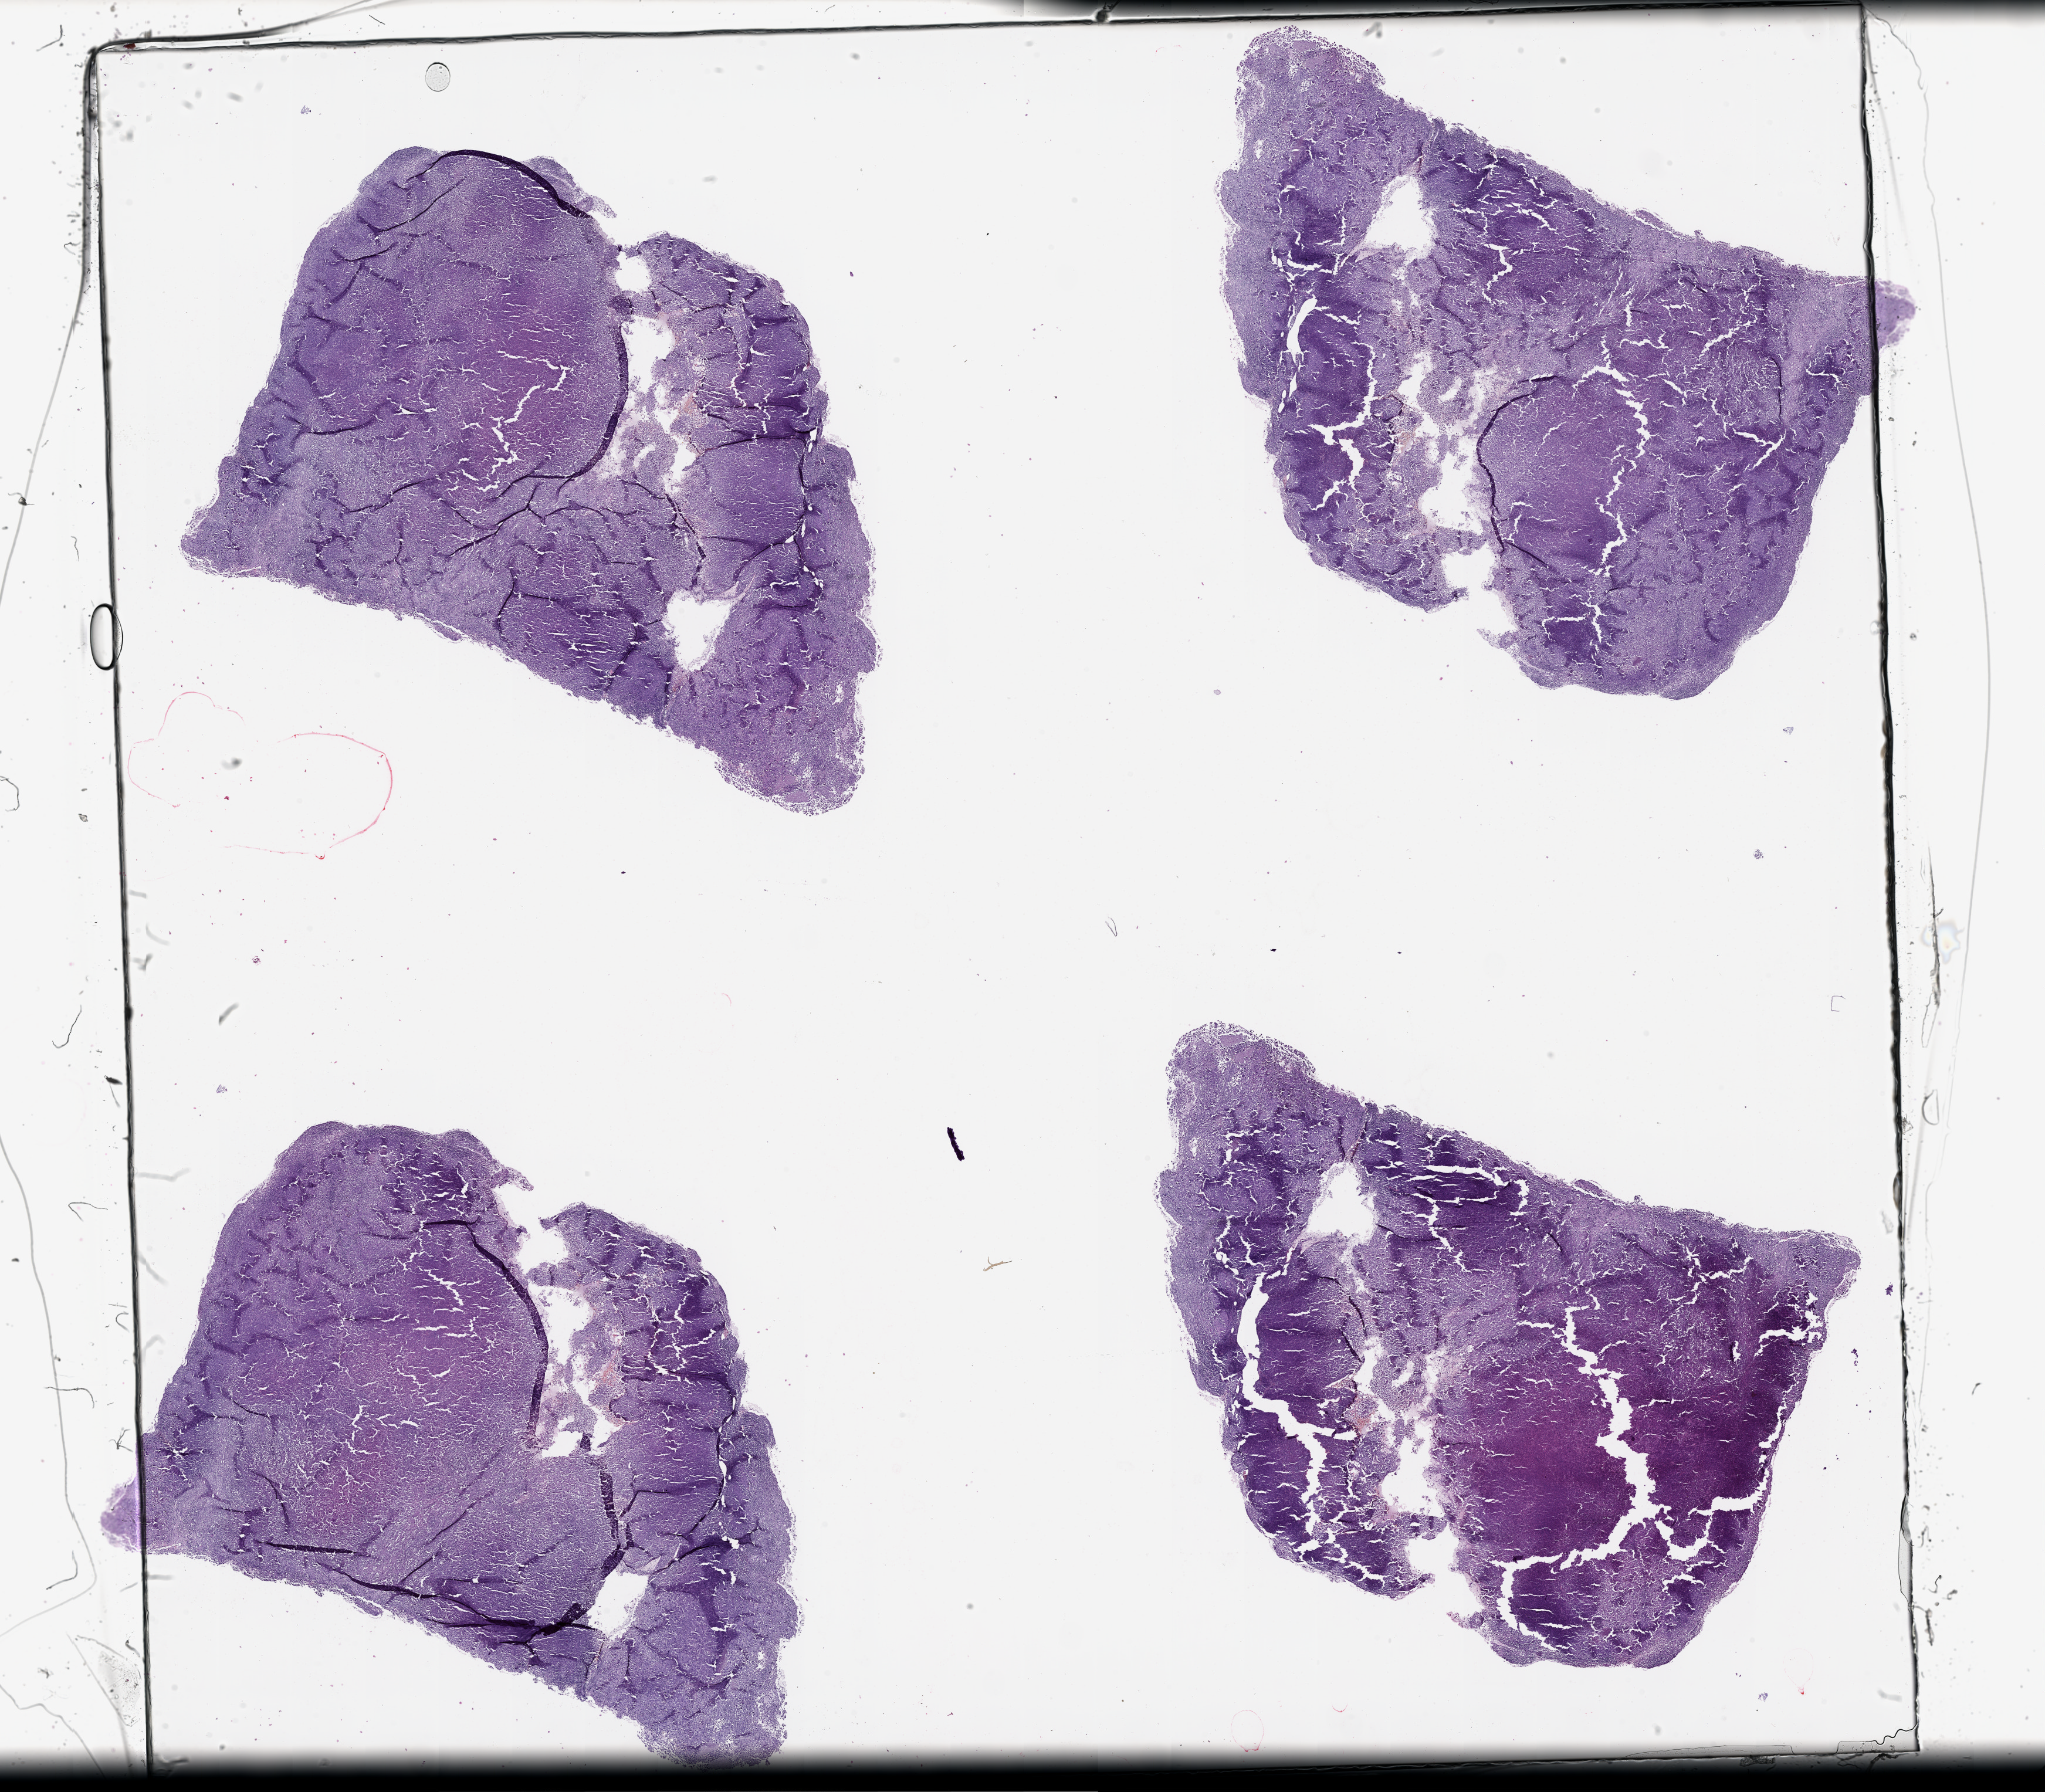
Digitized H&E tissue section (whole slide) — shown as a low-resolution overview of the whole scanned area (about 28.1 x 24.6 mm, acquisition: 20x scan). Patient: male, age 47 years.
Patient diagnosis: Malignant melanoma, NOS.